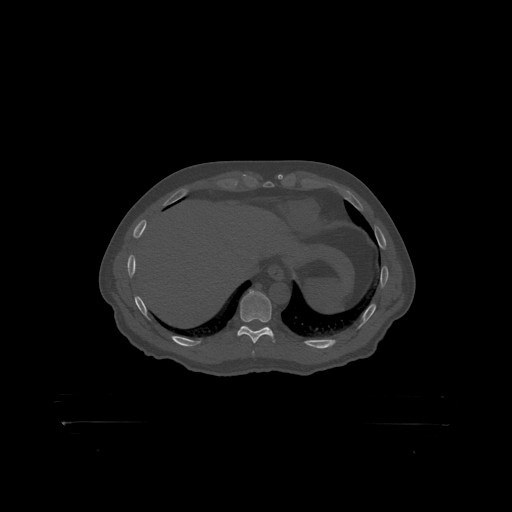
CT including the spine, one axial slice; position 398 of 399 along the scan axis; 120 kVp; bone window (W 1800 / L 400 HU); 512 × 512 image matrix. Male patient, age 46 years. Case-level facts recorded for this patient, not image findings: primary cancer: skin.
Structures marked on this image (semi-automatic segmentation, software-assisted and operator-edited):
- T10 vertebra: bounding box [x1, y1, x2, y2] px = [240, 290, 272, 319]